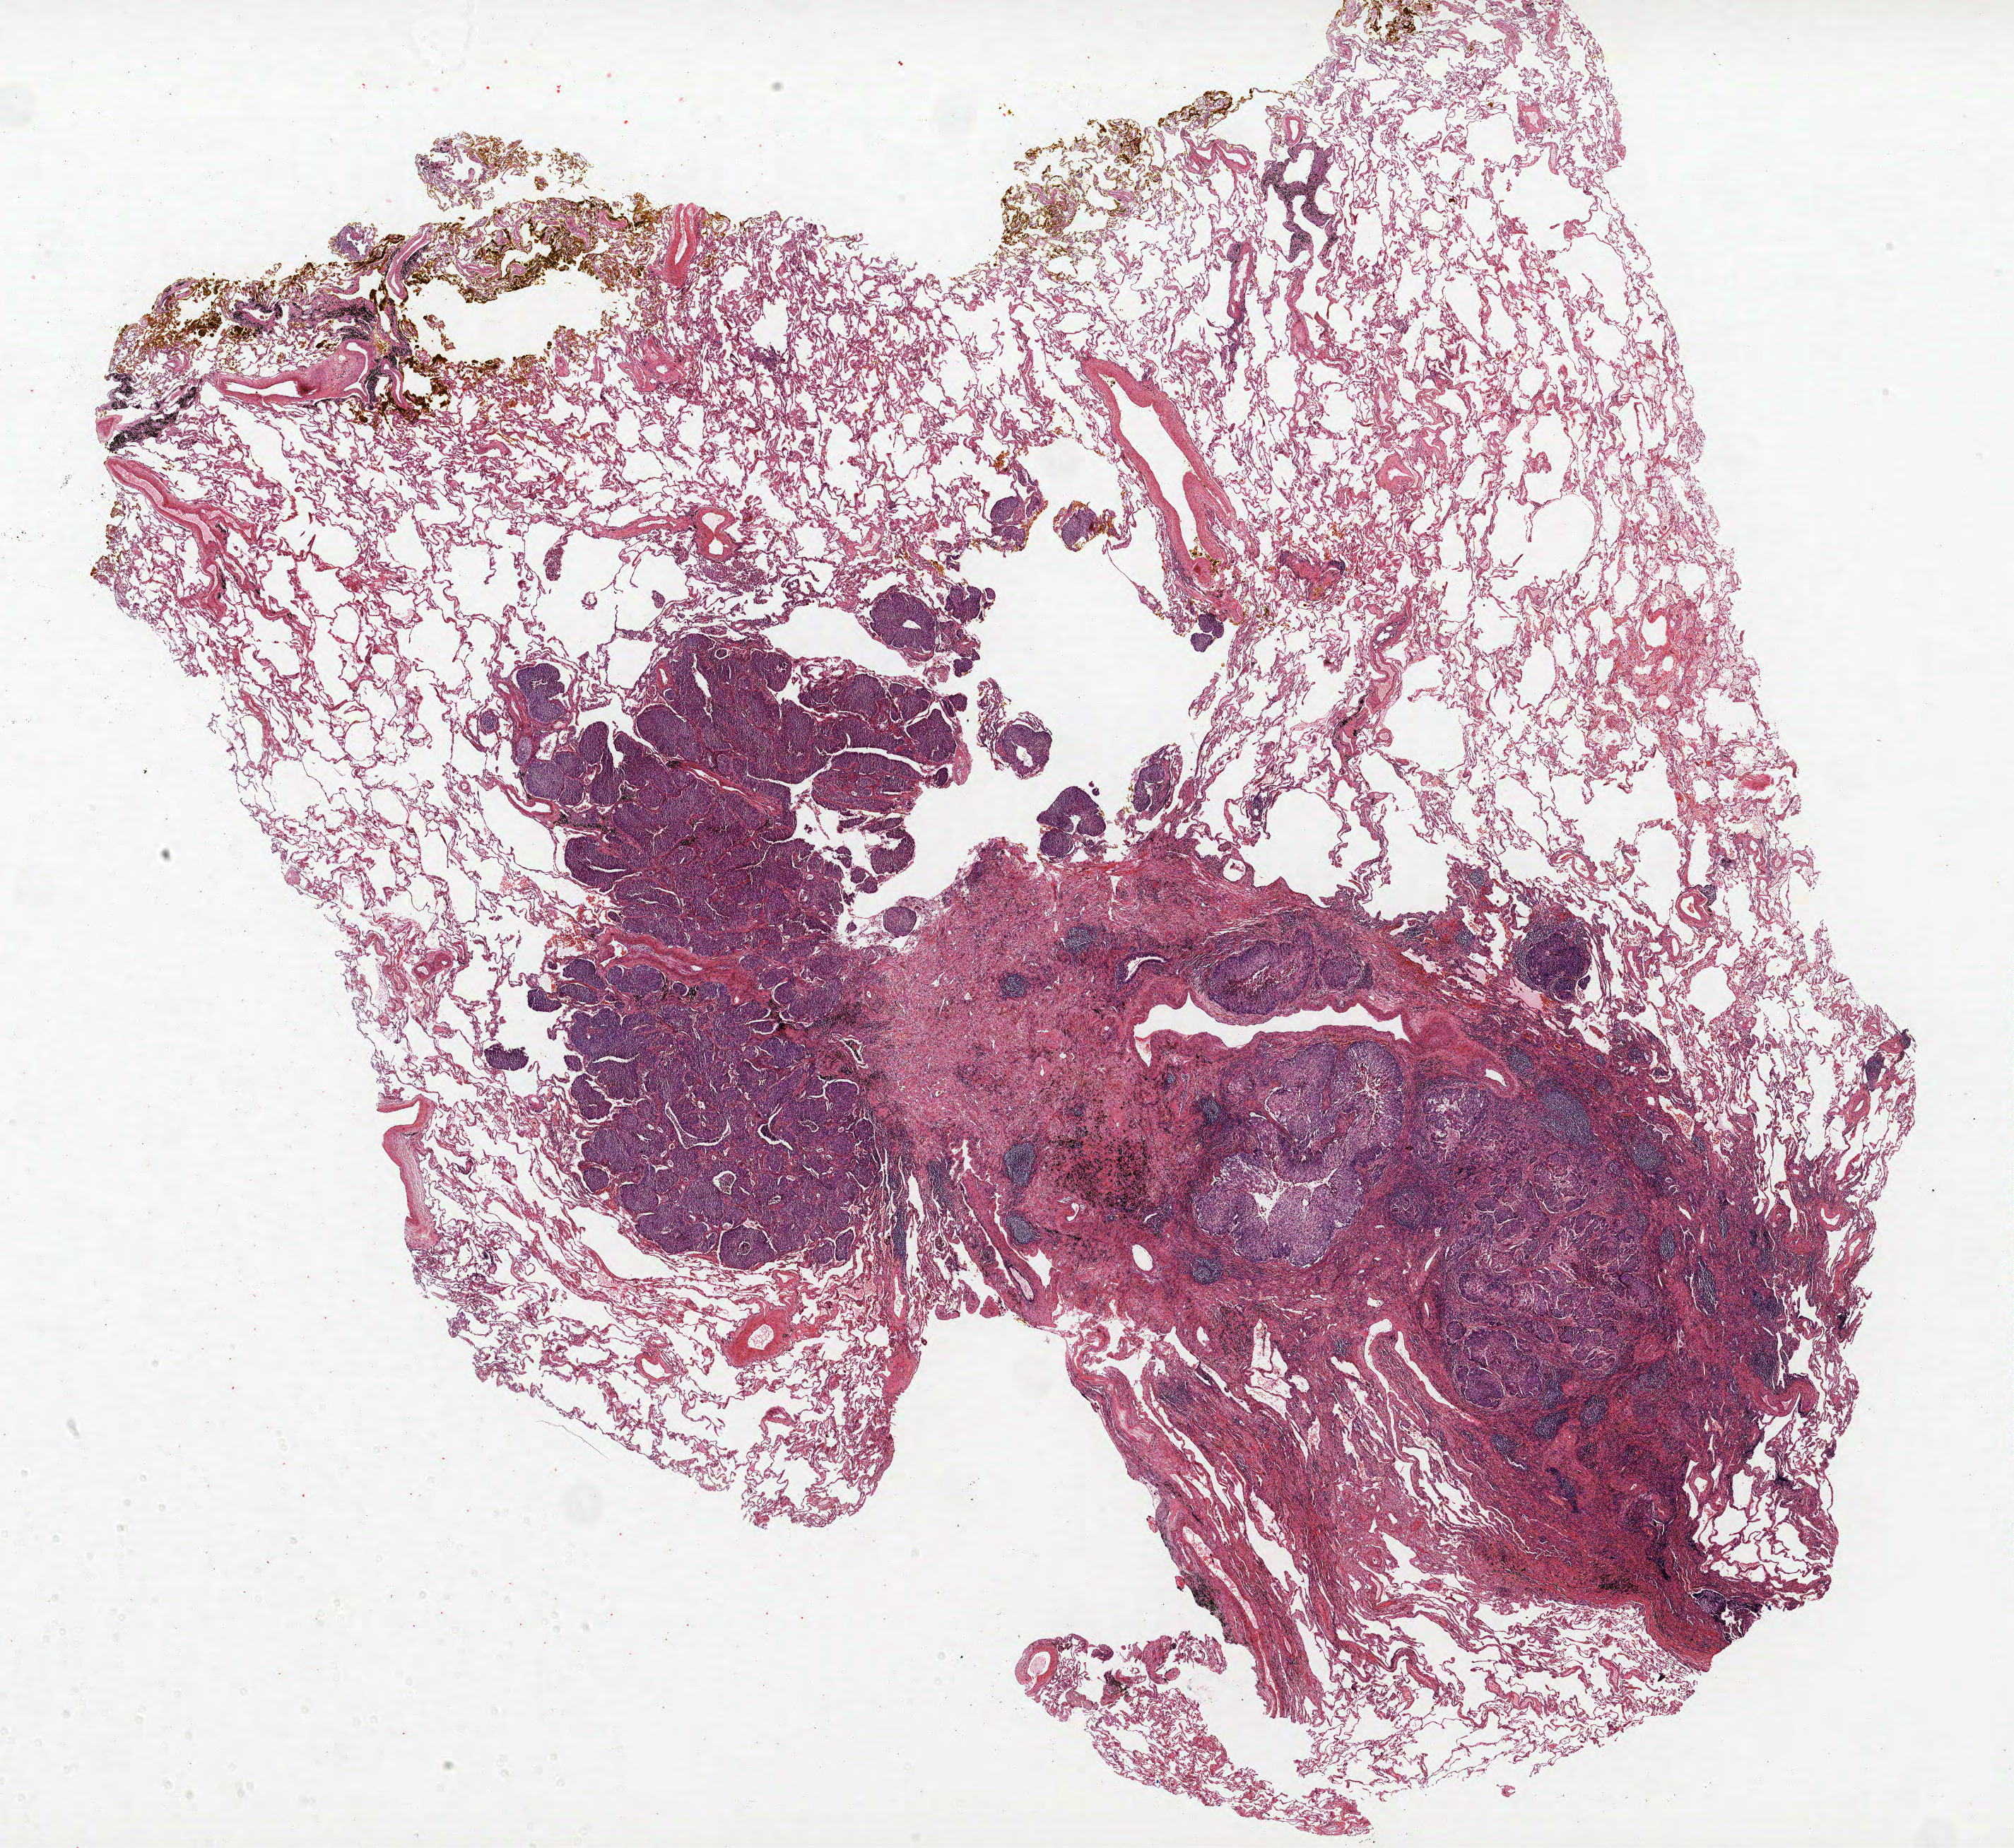
H&E-stained whole-slide image — whole scanned area (about 22.8 x 20.9 mm) shown as a low-resolution overview. FFPE section. Lung tissue. Female, age 70 at enrolment. Former smoker at enrolment.
Participant's lung-cancer diagnosis: Squamous cell carcinoma, NOS.